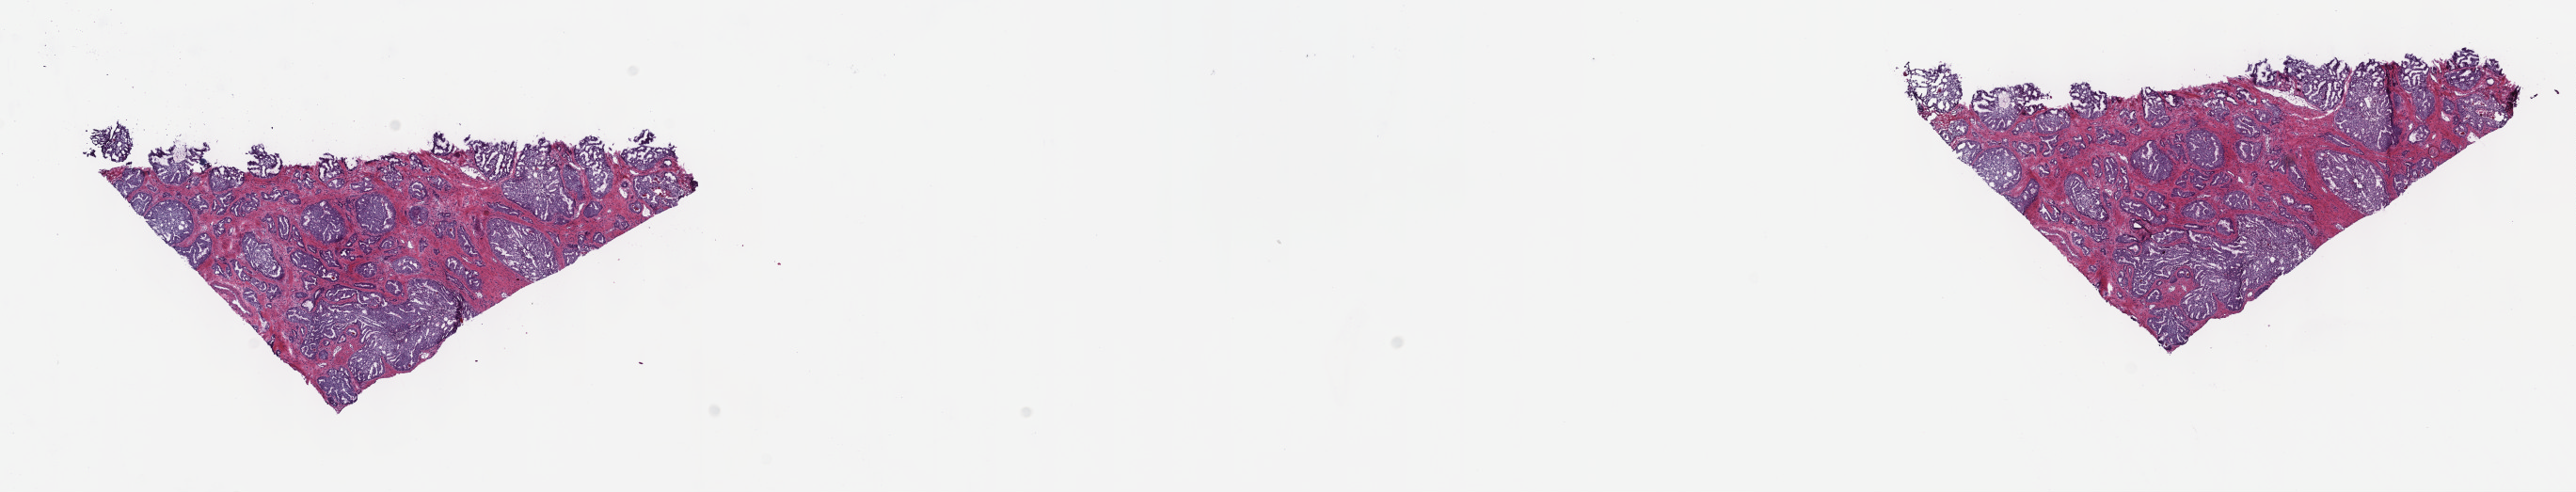
H&E-stained whole-slide image, a low-resolution overview of the entire scanned area, about 22.1 x 4.2 mm (slide scanned at 40x); frozen section from the top of the tissue portion; primary tumour sample from the prostate. Male patient; age at initial diagnosis 58 years. Gleason score: 9 (4+5). Slide review estimates, as recorded: tumour cells 80%, tumour nuclei 80%, normal cells 0%, stromal cells 20%, necrosis 0%. Infiltration values recorded for this section: lymphocyte infiltration 2%, monocyte infiltration 1%, neutrophil infiltration 1%.
Diagnosis: Adenocarcinoma, NOS. Lymph nodes positive (case pathology): 2 of 8 examined. Laterality: bilateral.